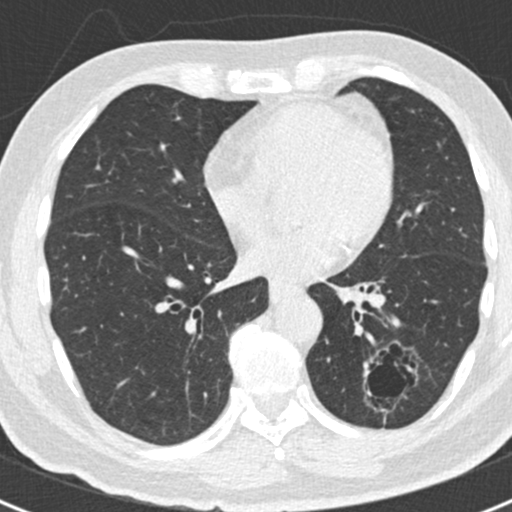
Chest CT (low-dose screening protocol), one axial image; first (baseline) screen; lung window (W 1500 / L -600 HU); 2 mm slice thickness; 120 kVp. Male, age 66 years at enrolment.
- Lesion marked by an expert reader, bounding box <344,339,420,417> (left, top, right, bottom; pixels).
- The exam's reader record, not a measurement of the box and not confirmed to be the same lesion: non-calcified nodule or mass ≥4 mm, left lower lobe, 43 × 27 mm, smooth margins.
- Participant outcome: lung cancer diagnosed 801 days after this screen (after the third annual screen) — adenocarcinoma, NOS, left lower lobe, poorly differentiated (G3), stage IB (AJCC 6th edition), 38 mm at pathology.